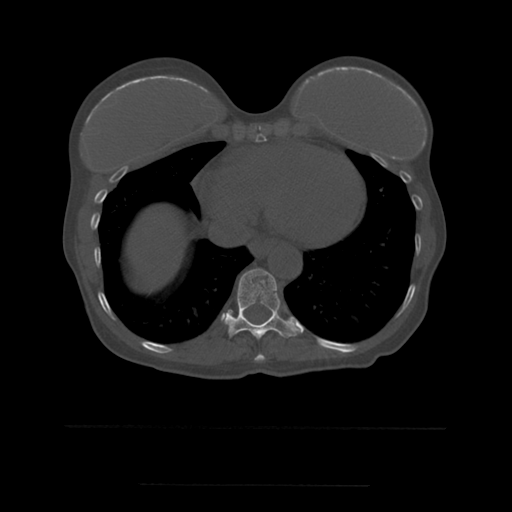
CT including the spine, one axial slice; slice 303 of 544 in the series (ordered by position); bone window (W 1800 / L 400 HU); 1.25 mm slice thickness; 512 × 512 image matrix, field of view 350 × 350 mm. Patient age 58 years. From the clinical record (not read from this slice): primary cancer: lung.
Structures marked on this image (semi-automatically segmented with operator editing):
- T10 vertebra: bounding box [x1, y1, x2, y2] px = [225, 269, 296, 339]
- T9 vertebra: [255, 354, 265, 361]